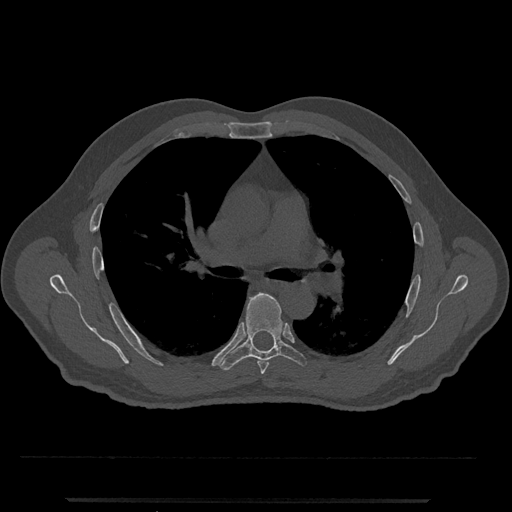
CT including the spine, one axial slice. Slice 752 of 797 in the series (ordered by position). Bone window (W 1800 / L 400 HU). 0.5 mm slice thickness. 512 × 512 image matrix, field of view 419 × 419 mm. Patient: male, 63 years. Case-level facts recorded for this patient, not image findings: primary cancer: prostate.
Outlined on this slice (semi-automatic segmentation, software-assisted and operator-edited):
- T5 vertebra: bounding box <257,360,269,375> (left, top, right, bottom; pixels)
- T6 vertebra: <219,292,307,371>